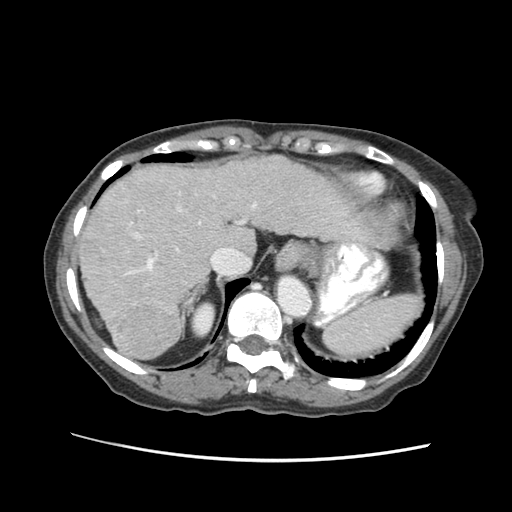
Contrast-enhanced abdominal CT (liver protocol), one axial slice; slice 45 of 63 in the series (ordered by position); 120 kVp; soft-tissue window (W 400 / L 40 HU); 2.5 mm slice thickness; 512 × 512 image matrix. From the clinical record (not read from this slice): diagnosis: hepatocellular carcinoma (patient treated with transarterial chemoembolisation; whether this scan precedes or follows treatment is not stated here); TNM stage (as recorded): Stage-I; Child-Pugh class: B.
Structures marked on this image (semi-automatic segmentation, software-assisted and operator-edited):
- liver parenchyma outside the tumour (the mass and vessels are separate outlines, so this box may not span the whole liver): bounding box (x1, y1, x2, y2) in pixels: (78, 152, 398, 360)
- mass: (114, 301, 178, 359)
- liver vessels: (128, 220, 240, 278)